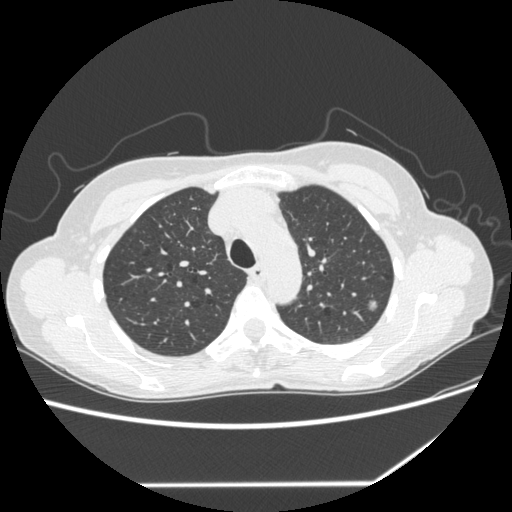
Chest CT (low-dose screening protocol), one axial image, second annual screen, lung window (W 1500 / L -600 HU), 1.25 mm slice thickness, standard (soft-tissue) reconstruction kernel (STANDARD), slice 57 of 255 in the series. Female, age 61 years at enrolment. Former smoker at enrolment.
- Expert reader's lesion annotation, box from (x=356, y=293) to (x=387, y=320) px.
- The exam's reader record, not a measurement of the box and not confirmed to be the same lesion: non-calcified nodule or mass ≥4 mm, left upper lobe, 8 × 7 mm, poorly defined margins, mixed attenuation, pre-existing on the prior screen: yes; interval growth: yes.
- Official screen result: positive, change unspecified: nodule(s) >= 4 mm or enlarging nodule(s), mass(es), or other non-specific abnormalities suspicious for lung cancer.
- Lung cancer was diagnosed 113 days after this screen: bronchiolo-alveolar adenocarcinoma, NOS, left upper lobe, well differentiated (G1), stage IA (AJCC 6th edition), 8 mm at pathology.